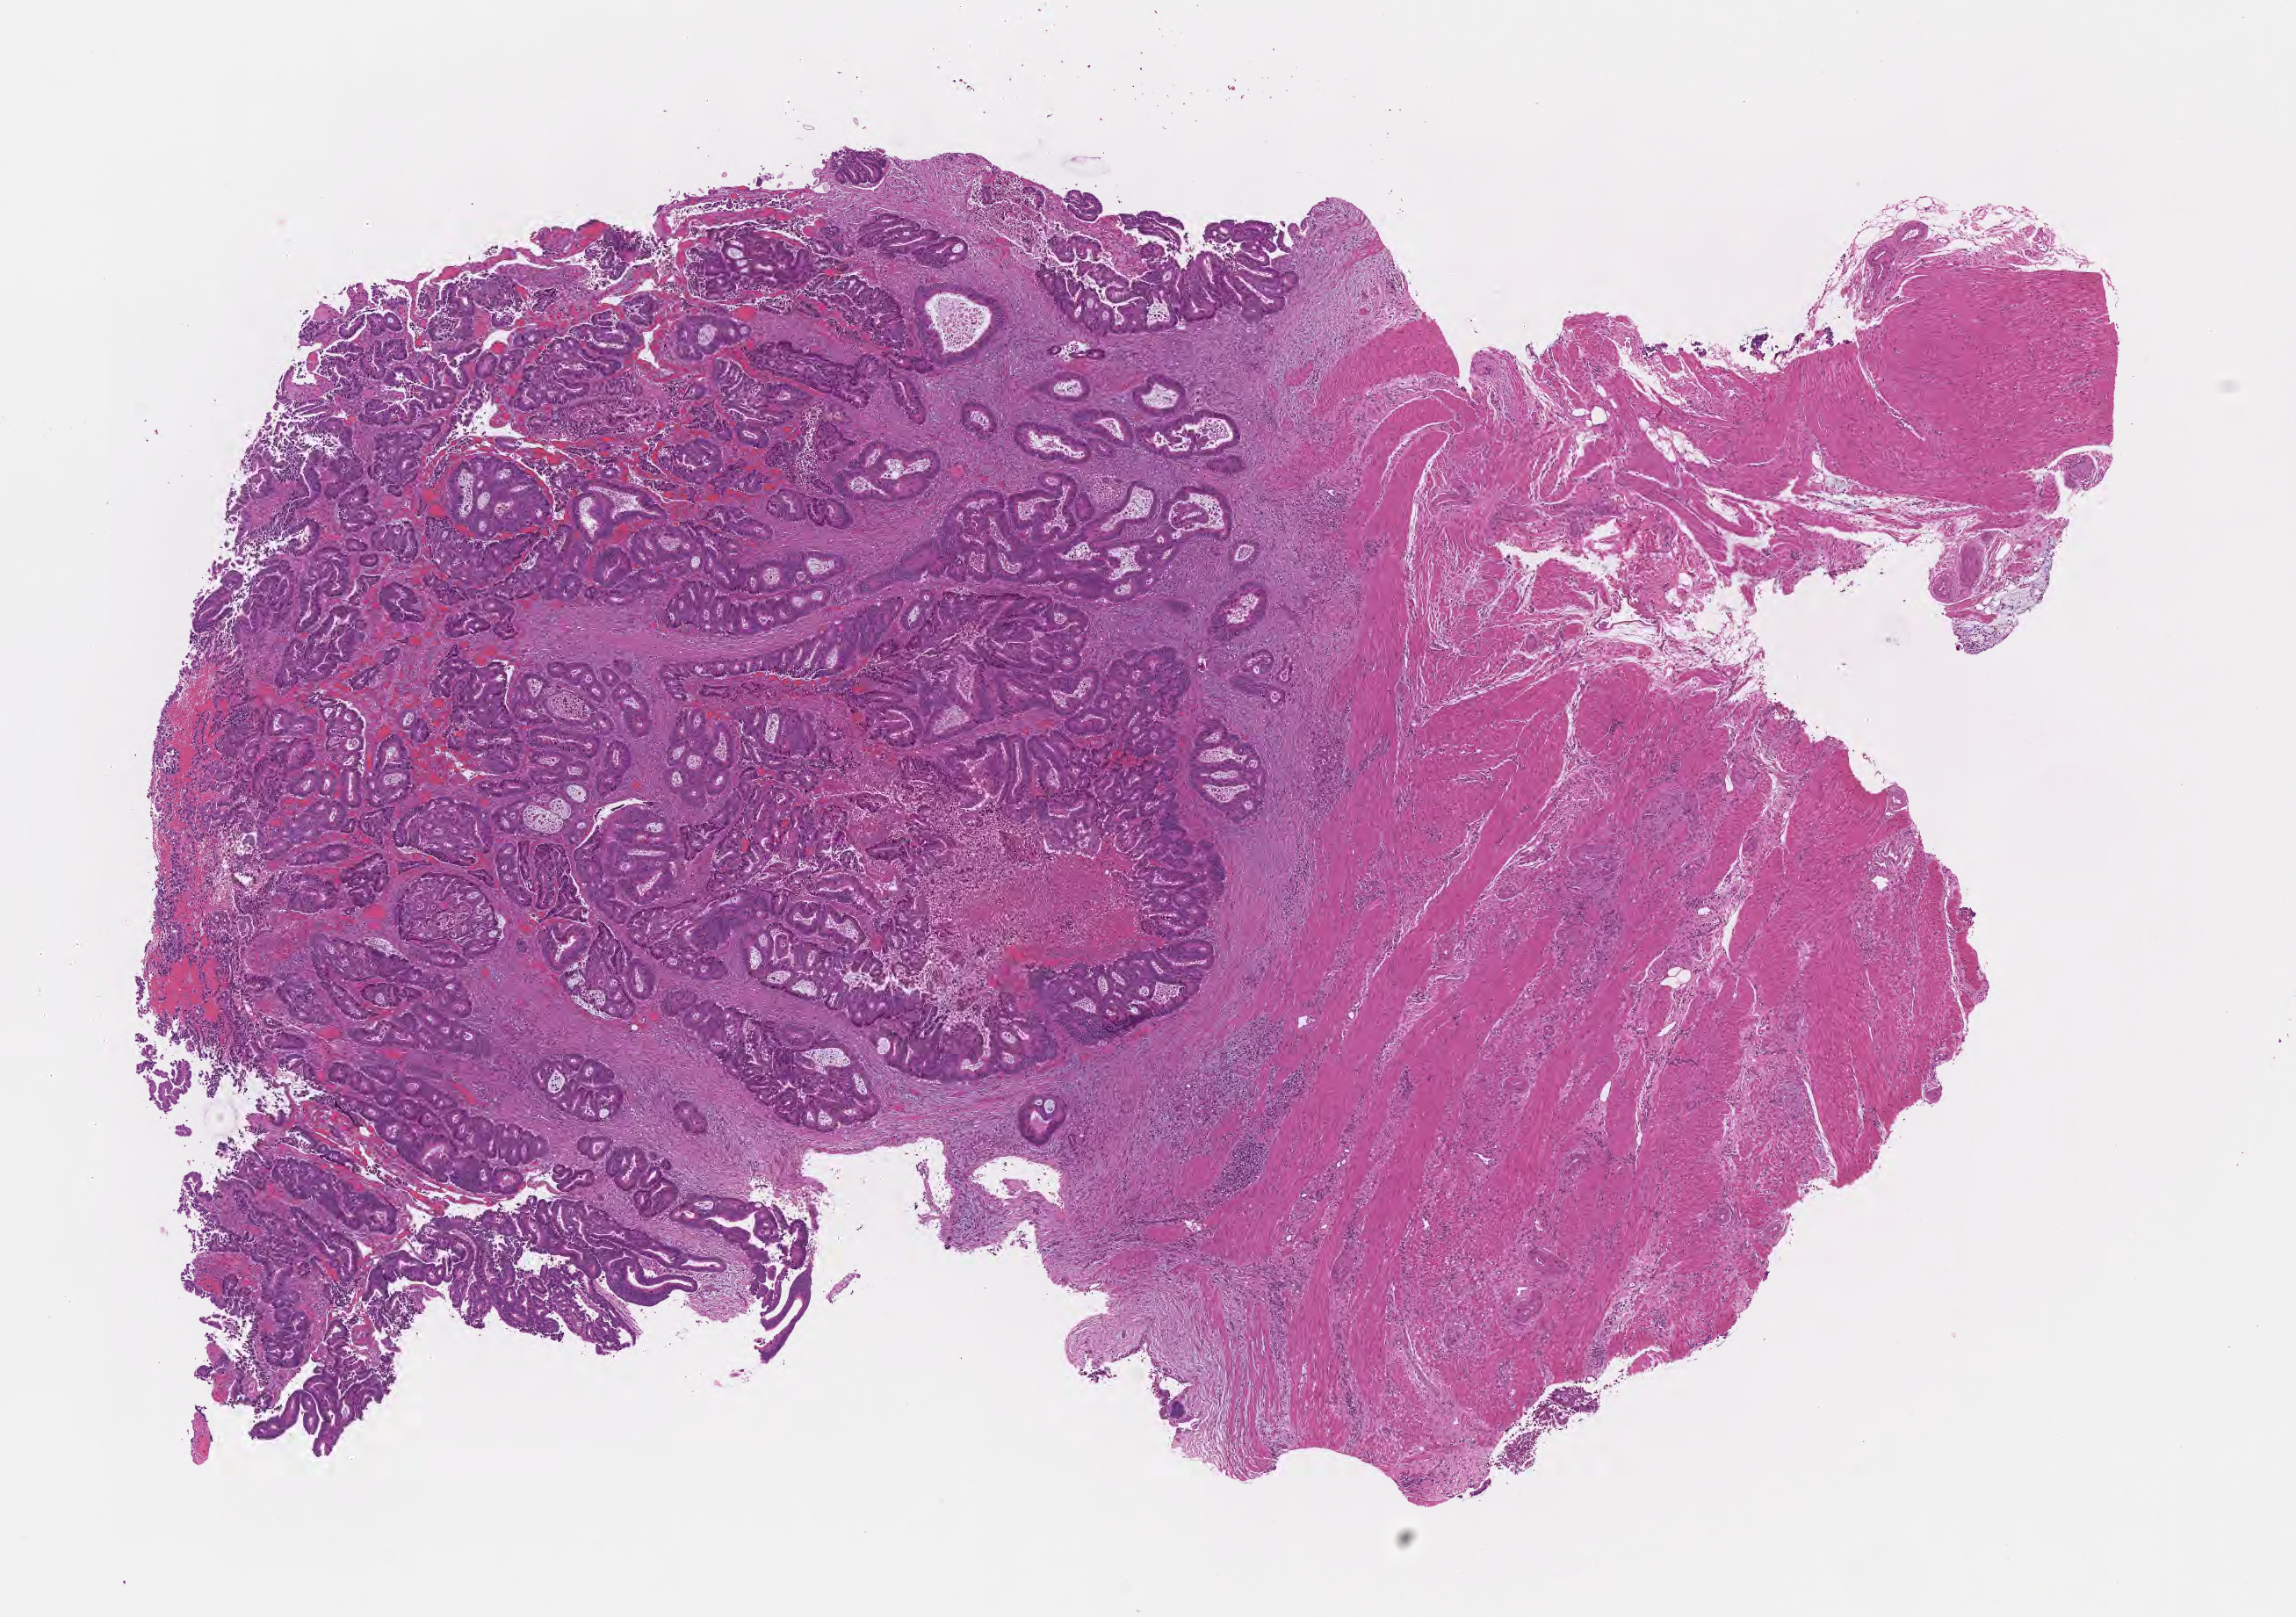
Digitized H&E-stained section — a low-resolution overview of the entire scanned area, about 10.6 x 7.4 mm; formalin-fixed, paraffin-embedded (FFPE) tissue; primary tumor; anatomic site: cecum. Male patient; age at initial diagnosis 71 years. Tumor grade: G2 (moderately differentiated). Pathologist review of this section (percent, as recorded): tumor cells 80%, tumor nuclei 80%, stromal cells 17%, necrosis 3%, normal cells 0%. Infiltration values recorded for this section: lymphocyte infiltration 5%, monocyte infiltration 1%, neutrophil infiltration 7%.
Diagnosis: Adenocarcinoma, NOS. AJCC pathologic stage: Stage IIA. Section: bottom of the tissue portion.